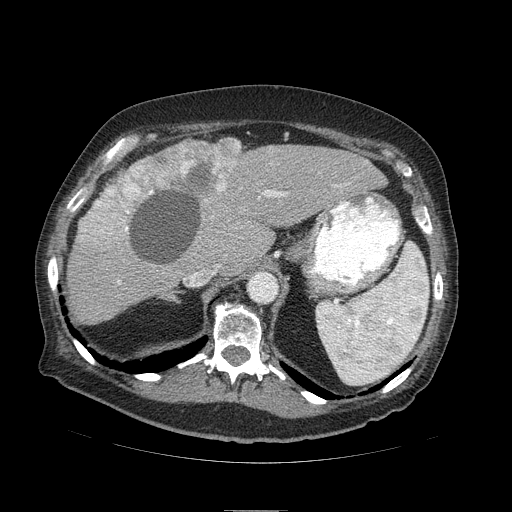
Contrast-enhanced abdominal CT (liver protocol), one axial slice; position 66 of 103 along the scan axis; soft-tissue window (W 400 / L 40 HU); 512 × 512 image matrix, field of view 440 × 440 mm. Case-level facts recorded for this patient, not image findings: diagnosis: hepatocellular carcinoma (patient treated with transarterial chemoembolisation; whether this scan precedes or follows treatment is not stated here); TNM stage (as recorded): Stage-IIIA; Child-Pugh class: B.
Structures marked on this image (semi-automatic segmentation, software-assisted and operator-edited):
- liver parenchyma outside the tumour (the mass and vessels are separate outlines, so this box may not span the whole liver): box from (x=66, y=138) to (x=387, y=324) px
- mass: (x=79, y=137)–(x=240, y=252)
- liver vessels: (x=195, y=192)–(x=283, y=275)